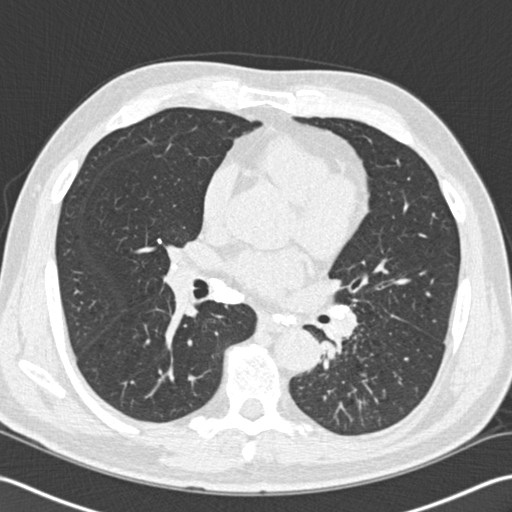
Low-dose screening chest CT, one axial slice. Slice 91 of 170 in the series (ordered by position). Lung window (W 1500 / L -600 HU). 2 mm slice thickness. 512 × 512 image matrix, field of view 350 × 350 mm.
Structures marked on this image (outlined manually by an expert reader):
- lesion 1 (tumor, lower lobe of left lung): bounding box [x1, y1, x2, y2] px = [320, 340, 337, 359]